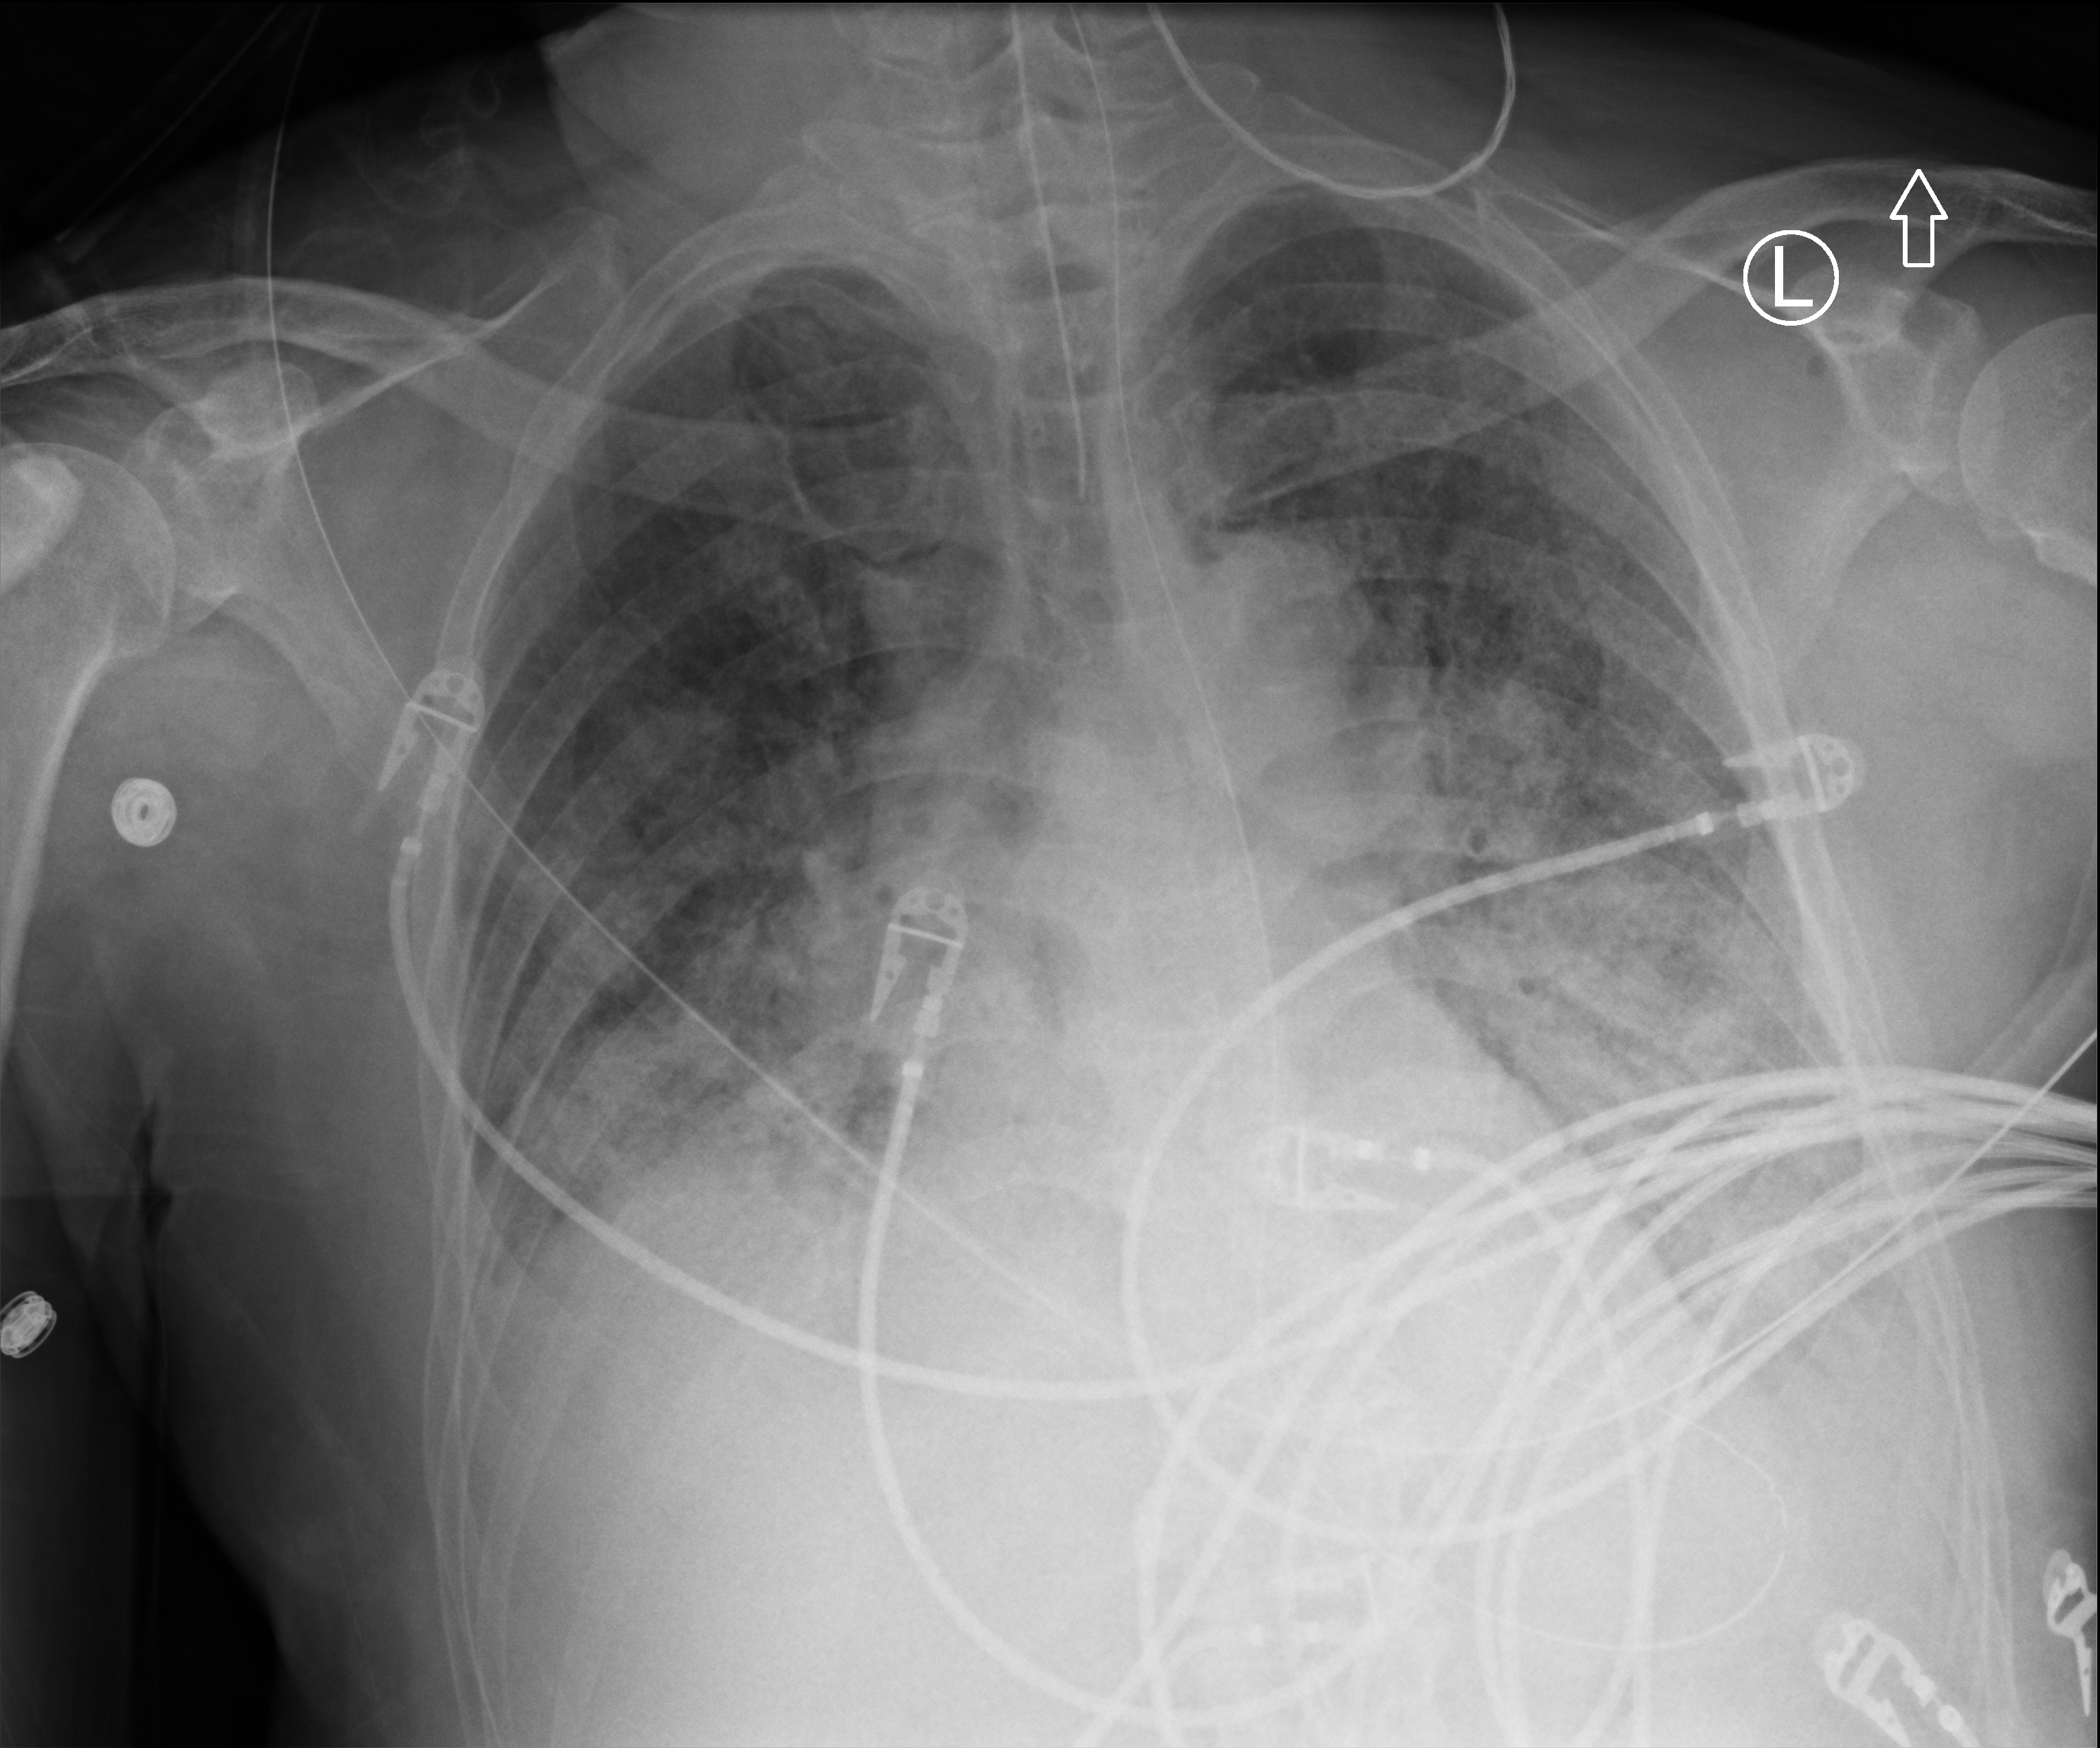
Portable chest radiograph, anteroposterior (AP) projection. Male patient hospitalised with COVID-19, age 60–74 years.
From the hospital-stay record, not from the radiograph (when in the stay this image was taken is not recorded): COPD (admission record): no; smoking status (admission record): former.